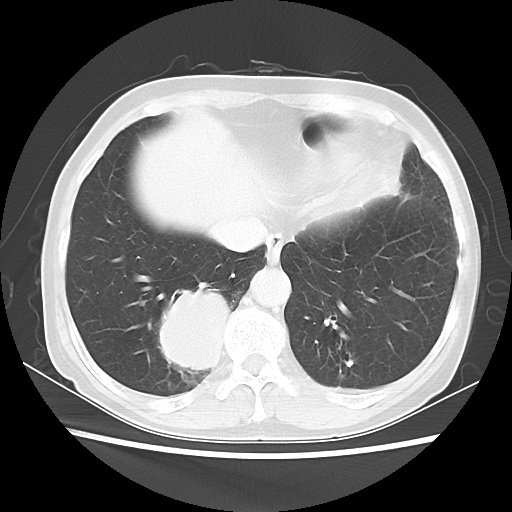
Chest CT, one axial slice; slice 14 of 56 in the series (ordered by position); 120 kVp; lung window (W 1500 / L -600 HU); 5 mm slice thickness; 512 × 512 image matrix, field of view 332 × 332 mm. Patient: female, 66 years. From the clinical record (not read from this slice): clinical TNM (as recorded): T2 N3 M0.
Outlined on this slice (bounding box drawn by a radiologist):
- lung tumour (recorded histology: small cell carcinoma): bounding box <153,280,241,383> (left, top, right, bottom; pixels)